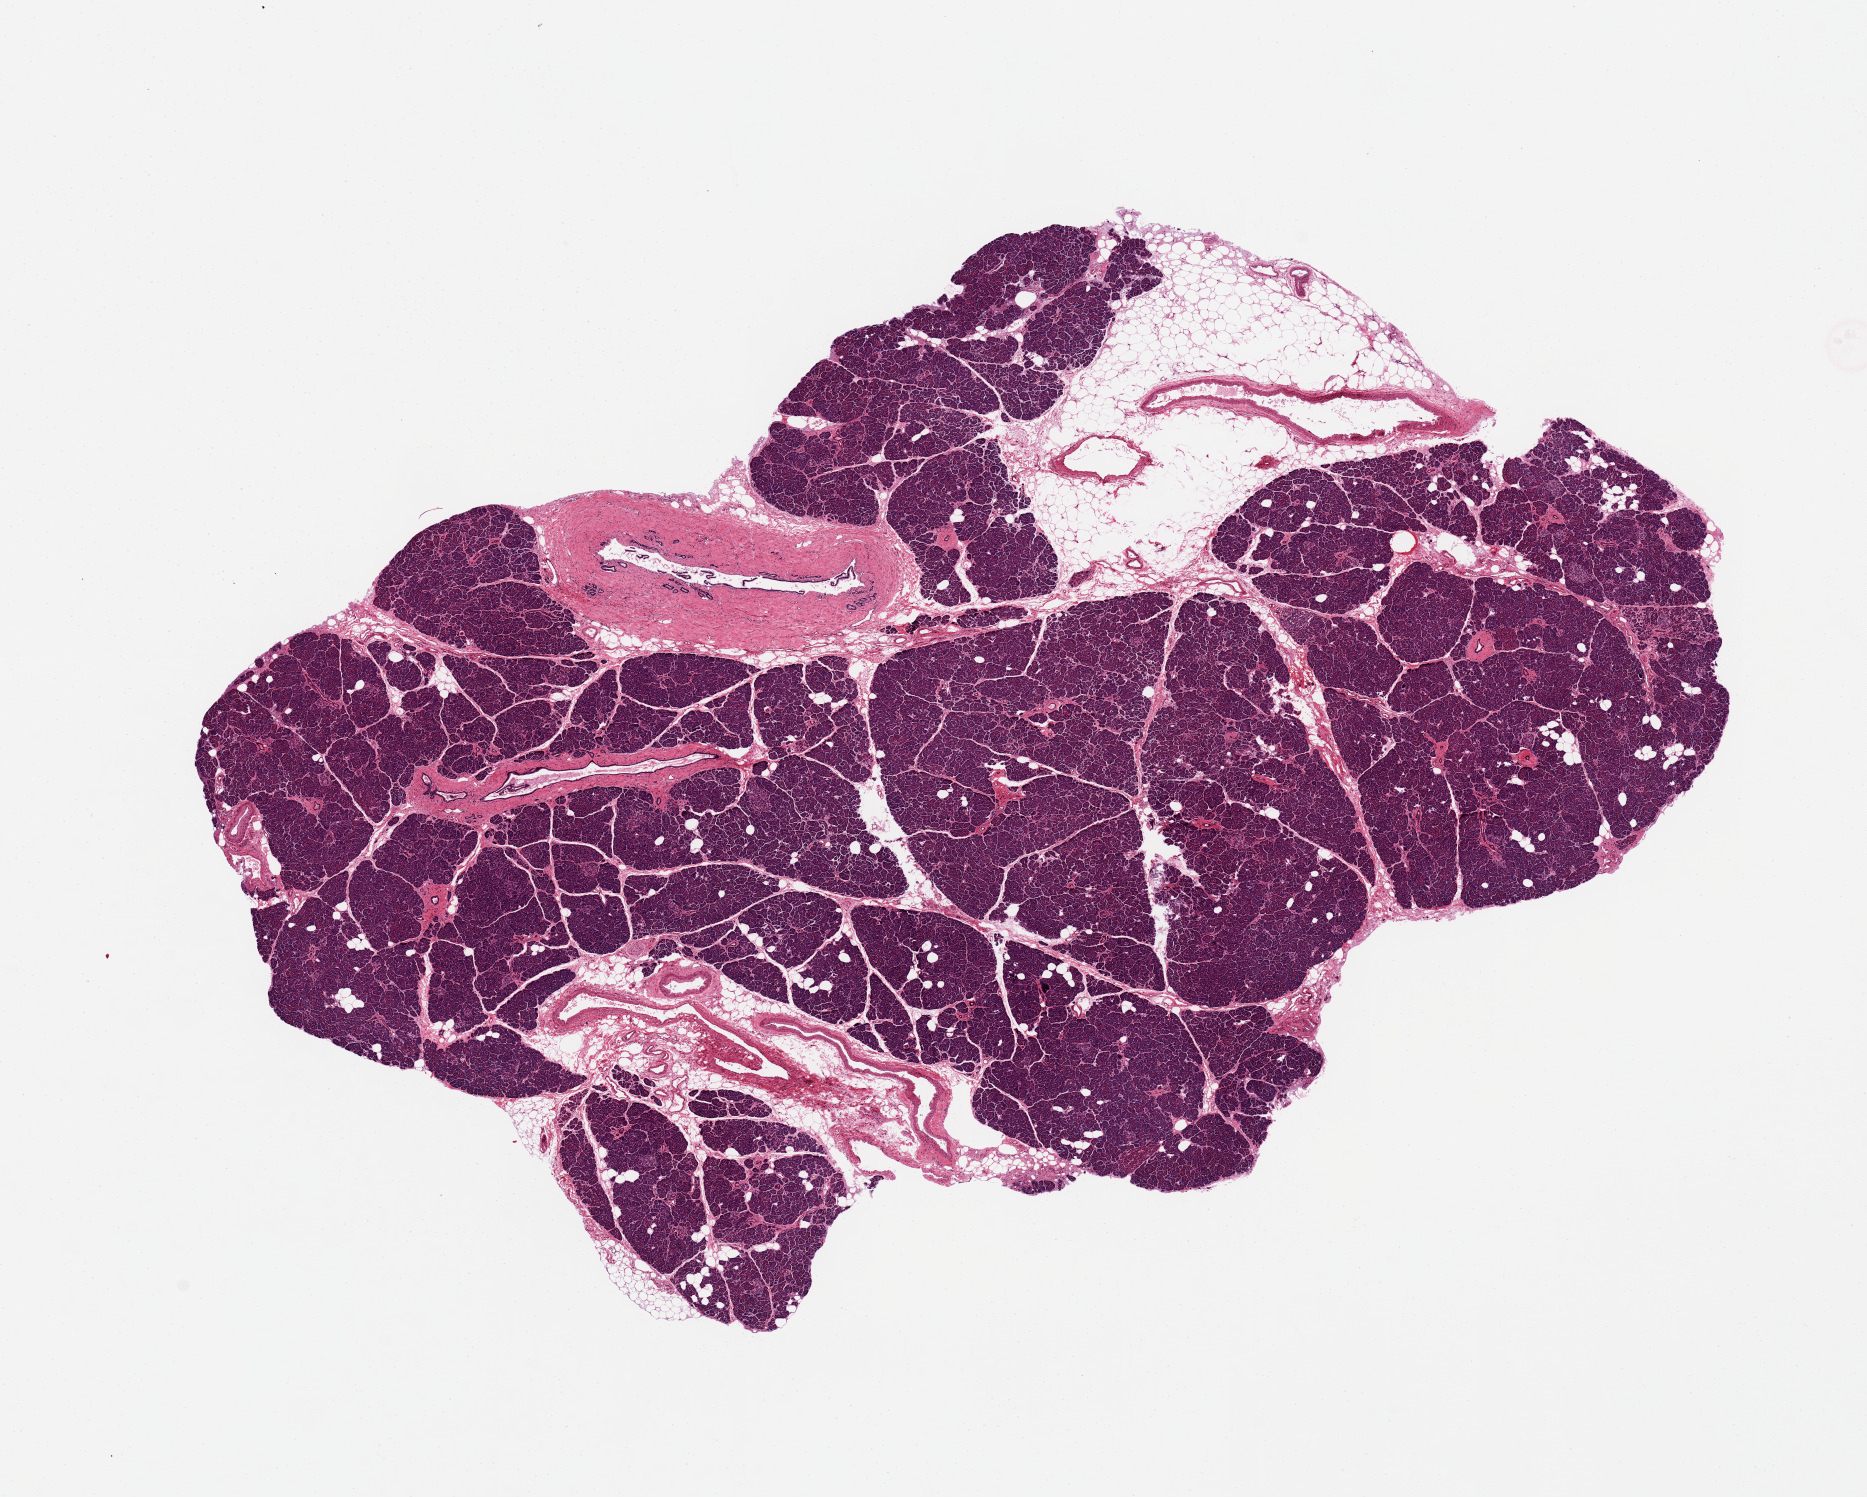
Digitized haematoxylin and eosin-stained section, brightfield, shown as a low-resolution overview of the whole scanned area (about 14.8 x 11.8 mm); PAXgene-fixed paraffin-embedded (PFPE) section; section of pancreas (target tissue); tissue donor sample. Male donor.
Review note (as recorded): Remarkably well preserved parenchyma. 12 x 6.9mm aliquot, 80% parenchyma.